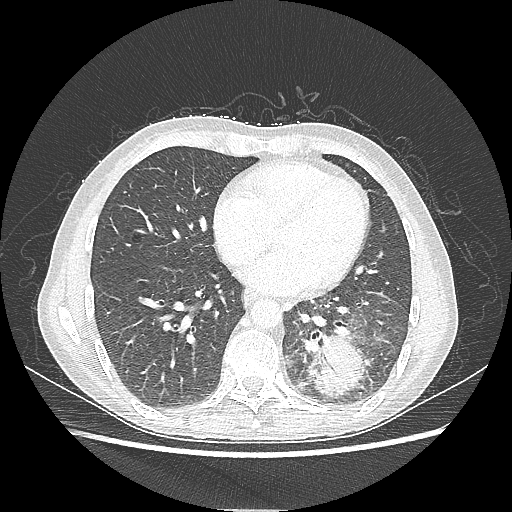
Chest CT, one axial slice. Position 87 of 220 along the scan axis. Reconstruction kernel LUNG. 80 kVp. Lung window (W 1500 / L -600 HU). 1.25 mm slice thickness. 512 × 512 image matrix, field of view 360 × 360 mm. Patient: female, 53 years. From the clinical record (not read from this slice): clinical TNM (as recorded): T3 N0 M0.
Annotated regions visible in this slice (rectangle marked by the reading radiologist):
- lung tumour (recorded histology: adenocarcinoma): bounding box [x1, y1, x2, y2] px = [298, 328, 370, 399]